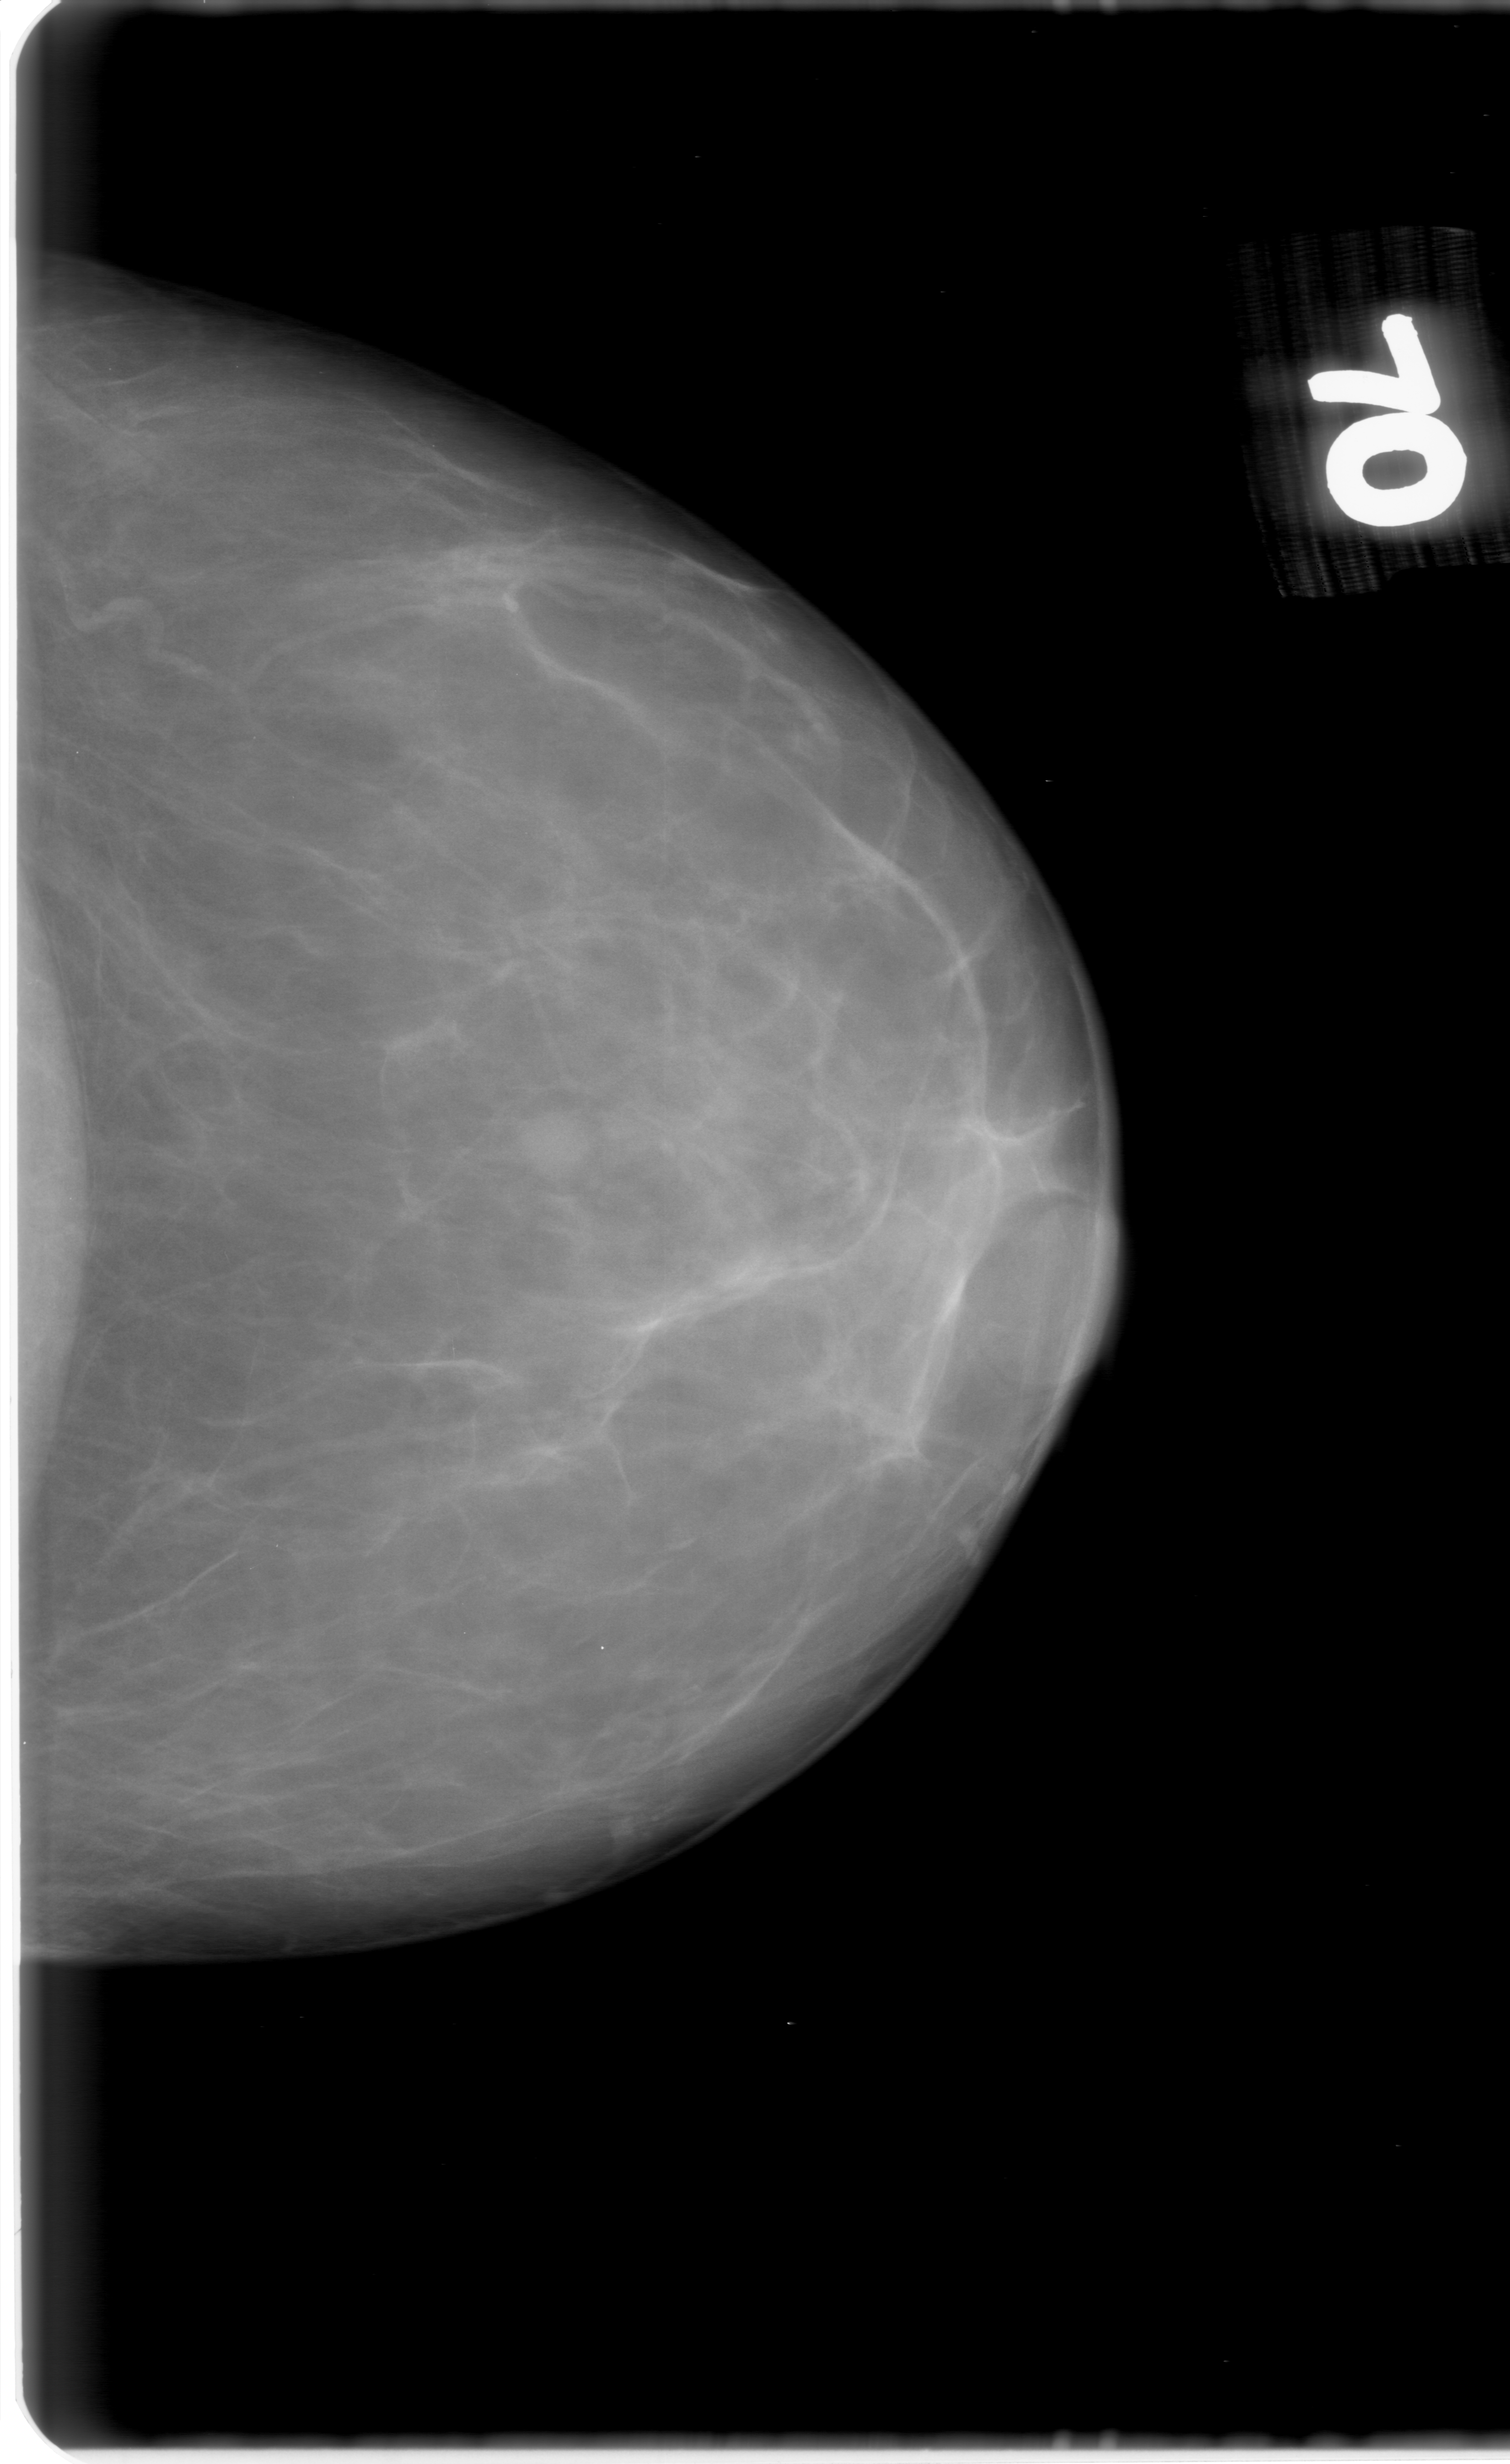
Digitized screen-film mammogram. Left breast. CC view. BI-RADS breast density category 1 (scale 1–4). 1510 × 2464 image matrix.
Marked abnormalities (boxes around the expert regions of interest):
- mass, shape round, margins obscured; BI-RADS assessment category 0; subtlety rating 4 on a 1 (subtle) to 5 (obvious) scale; pathology result (as recorded, not read from the image): benign: bounding box <482,1073,611,1189> (left, top, right, bottom; pixels)